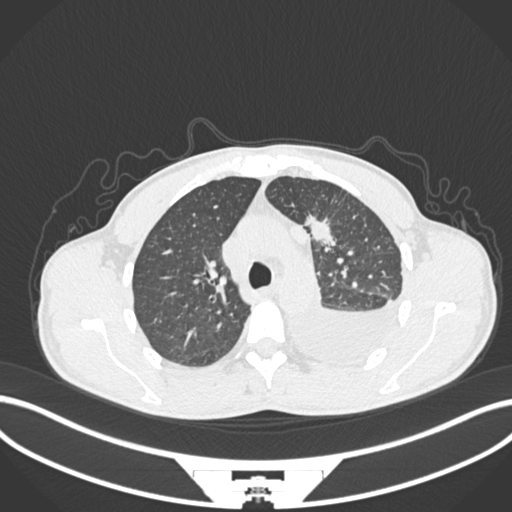
Chest CT, one axial slice; position 154 of 244 along the scan axis; reconstruction kernel B30f; lung window (W 1500 / L -600 HU); 512 × 512 image matrix, field of view 400 × 400 mm. Male patient, age 49 years. Case-level facts recorded for this patient, not image findings: clinical TNM (as recorded): T1c N1 M1.
Annotated regions visible in this slice (rectangle marked by the reading radiologist):
- lung tumour (recorded histology: adenocarcinoma): bounding box <308,211,340,250> (left, top, right, bottom; pixels)